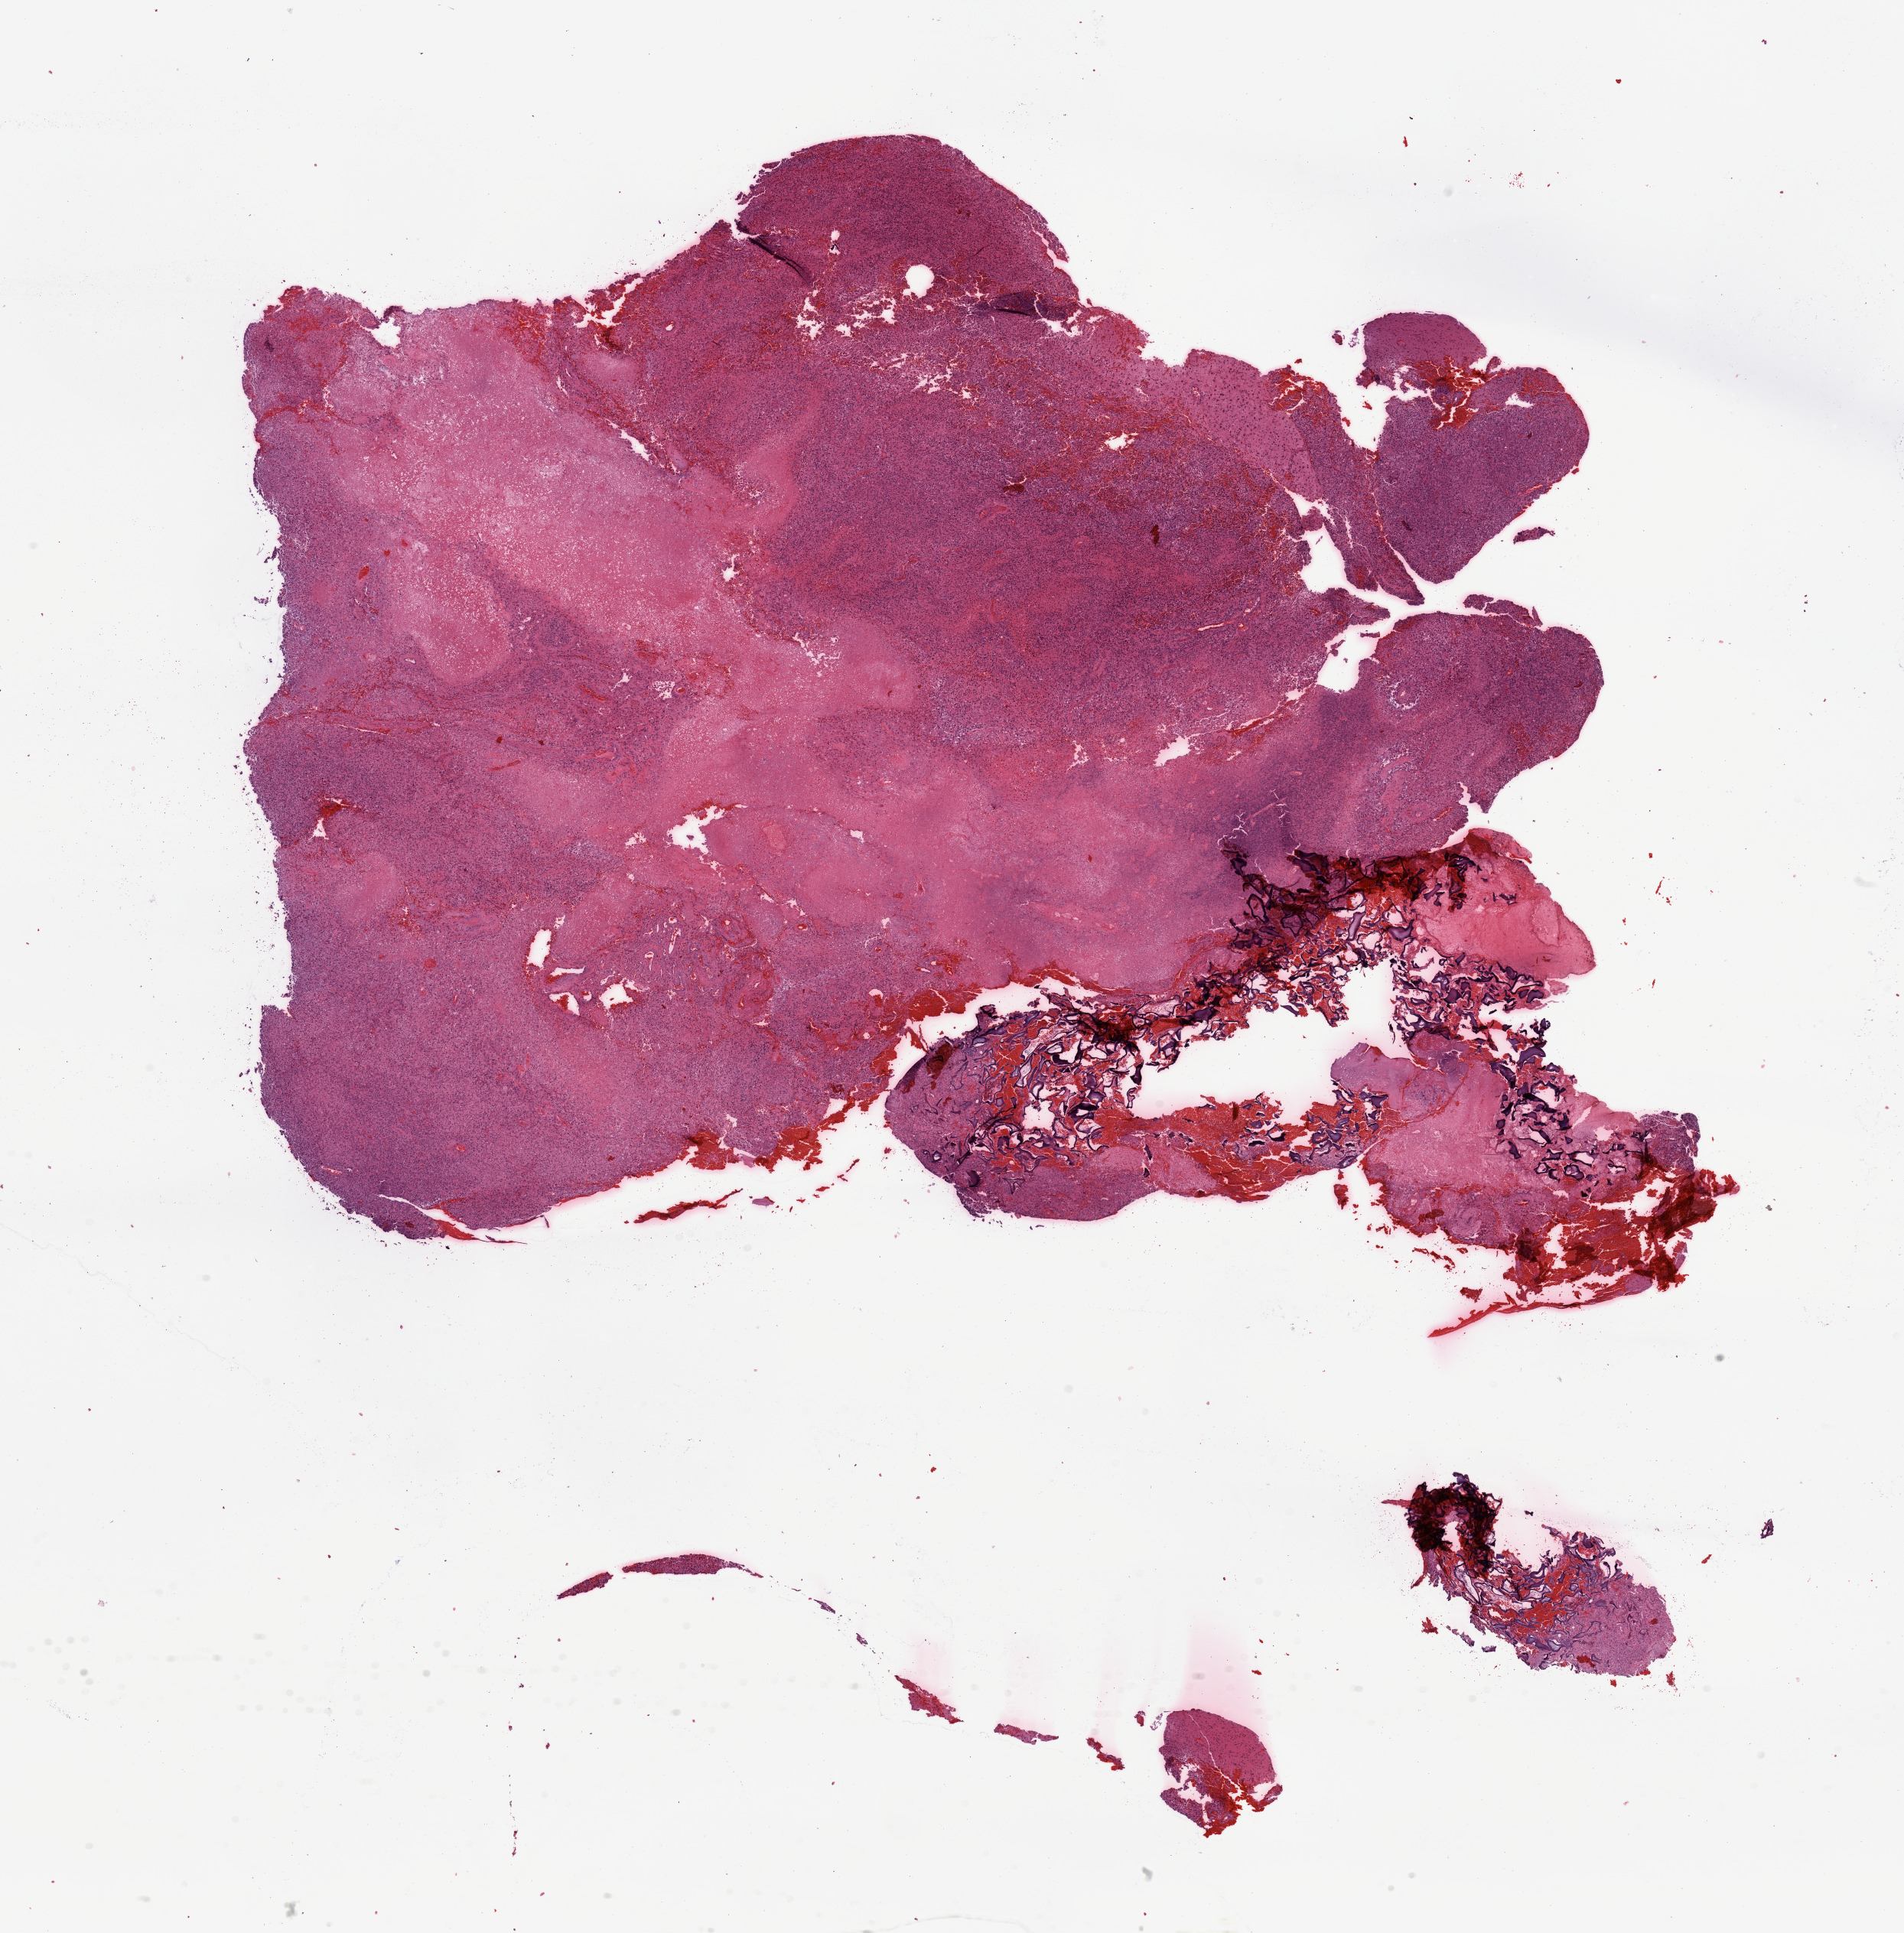
H&E whole-slide image — whole scanned area (about 19.7 x 20.0 mm, from a 20x scan) shown as a low-resolution overview; tumour tissue sample, sampled site: frontal lobe. 60-year-old male patient. Pathologist review of this section (percent, as recorded): tumour nuclei 75%, necrosis 25%.
• diagnosis: Glioblastoma
• primary tumour site (as recorded): frontal lobe